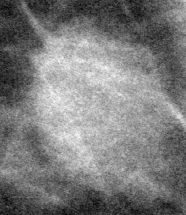
Crop from a digitized film mammogram around one marked abnormality; left breast; CC view; BI-RADS breast density category 2 (scale 1–4).
- Marked abnormality: mass, shape oval, margins circumscribed; BI-RADS assessment category 3; subtlety rating 5 on a 1 (subtle) to 5 (obvious) scale; pathology (as recorded): benign.